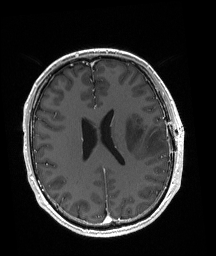
Brain MRI from a brain-tumour surgery series, one axial slice; T1-weighted post-contrast; 1 mm slice thickness; 216 × 256 image matrix, field of view 211 × 250 mm. From the clinical record (not read from this slice): histopathology: Astrocytoma; WHO grade: 3; IDH mutation: yes.
Outlined on this slice (outlined manually by an expert reader):
- tumour: bounding box [x1, y1, x2, y2] px = [125, 117, 167, 155]